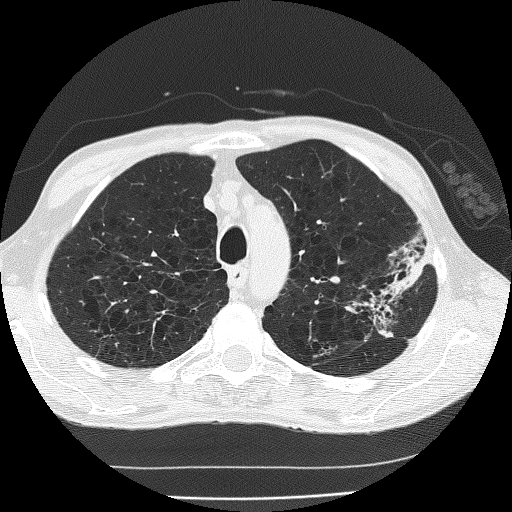
Chest CT (low-dose screening protocol), one axial image, second annual screen, lung window (W 1500 / L -600 HU), lung (sharp) reconstruction kernel (FC51), 512 × 512 image matrix. Male, age 60 years at enrolment.
Lesion marked by an expert reader, bounding box [x1, y1, x2, y2] px = [346, 249, 436, 338]. The screening reader recorded 2 non-calcified nodules or masses ≥4 mm on this exam; which of them this box marks is not recorded.